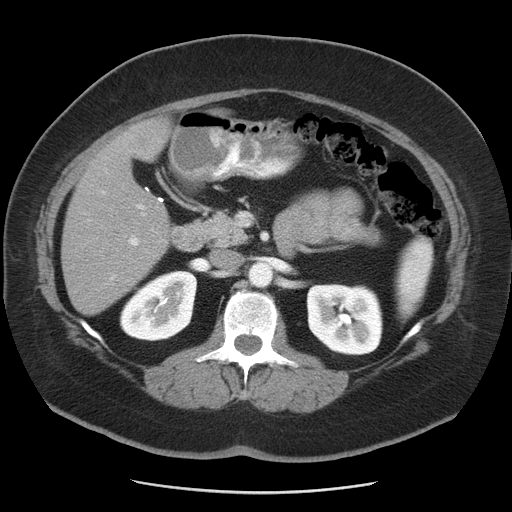
Contrast-enhanced abdominal CT, one axial slice. Position 22 of 55 along the scan axis. 120 kVp. Intravenous contrast given. Soft-tissue window (W 400 / L 40 HU). 5 mm slice thickness. 512 × 512 image matrix, field of view 380 × 380 mm. Female patient, age 52 years. From the clinical record (not read from this slice): diagnosis: colorectal cancer liver metastases, imaged before liver resection; multiple liver metastases: yes; largest metastasis: 2.5 cm; disease in both lobes: yes.
Outlined on this slice (outlined manually by an expert reader):
- liver: bounding box (x1, y1, x2, y2) in pixels: (62, 119, 172, 315)
- planned liver remnant (the part of the liver to remain after resection): (61, 190, 171, 315)
- portal vein (with intrahepatic branches): (98, 168, 153, 278)
- liver metastasis: (130, 129, 156, 151)